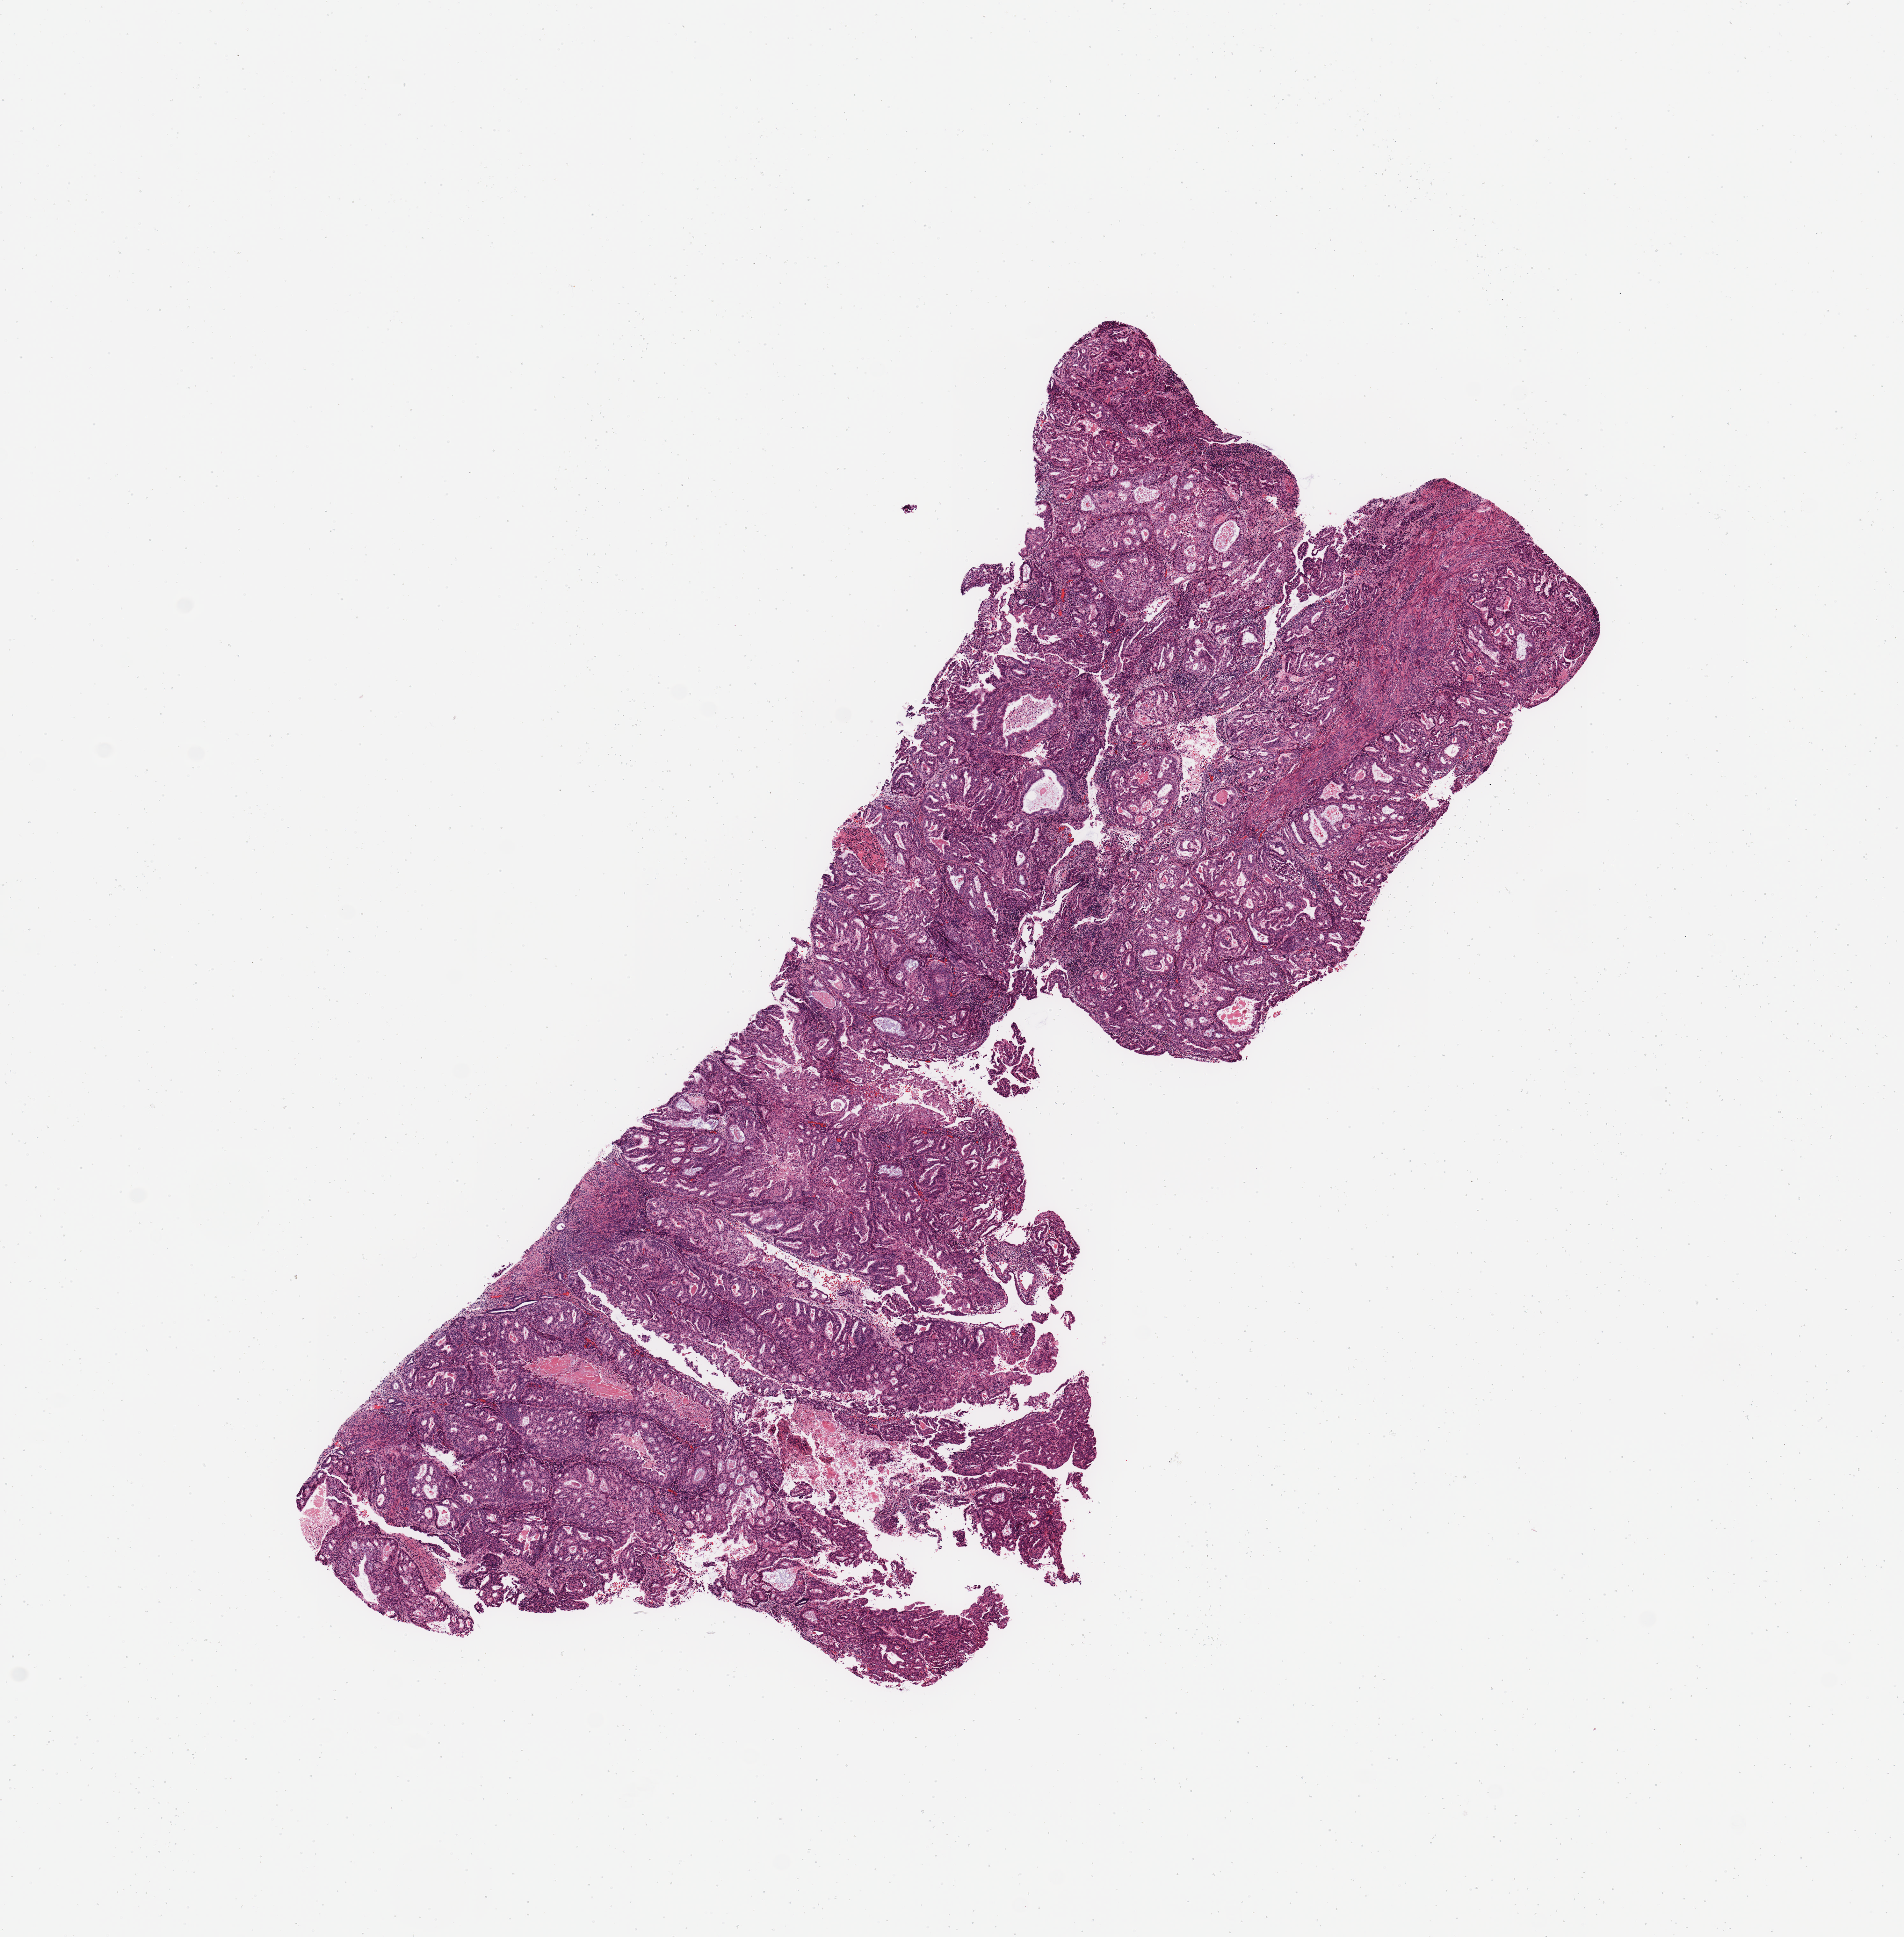
Digitized H&E-stained tissue section (whole slide) — a low-resolution overview of the entire scanned area, about 11.8 x 12.0 mm (slide scanned at 20x). Tumour tissue sample, sampled site: uterus. 66-year-old female patient. Pathologist review of this section (percent, as recorded): tumour nuclei 85%, necrosis 5%.
AJCC pathologic stage: II. Histologic diagnosis: Endometrioid adenocarcinoma, NOS.